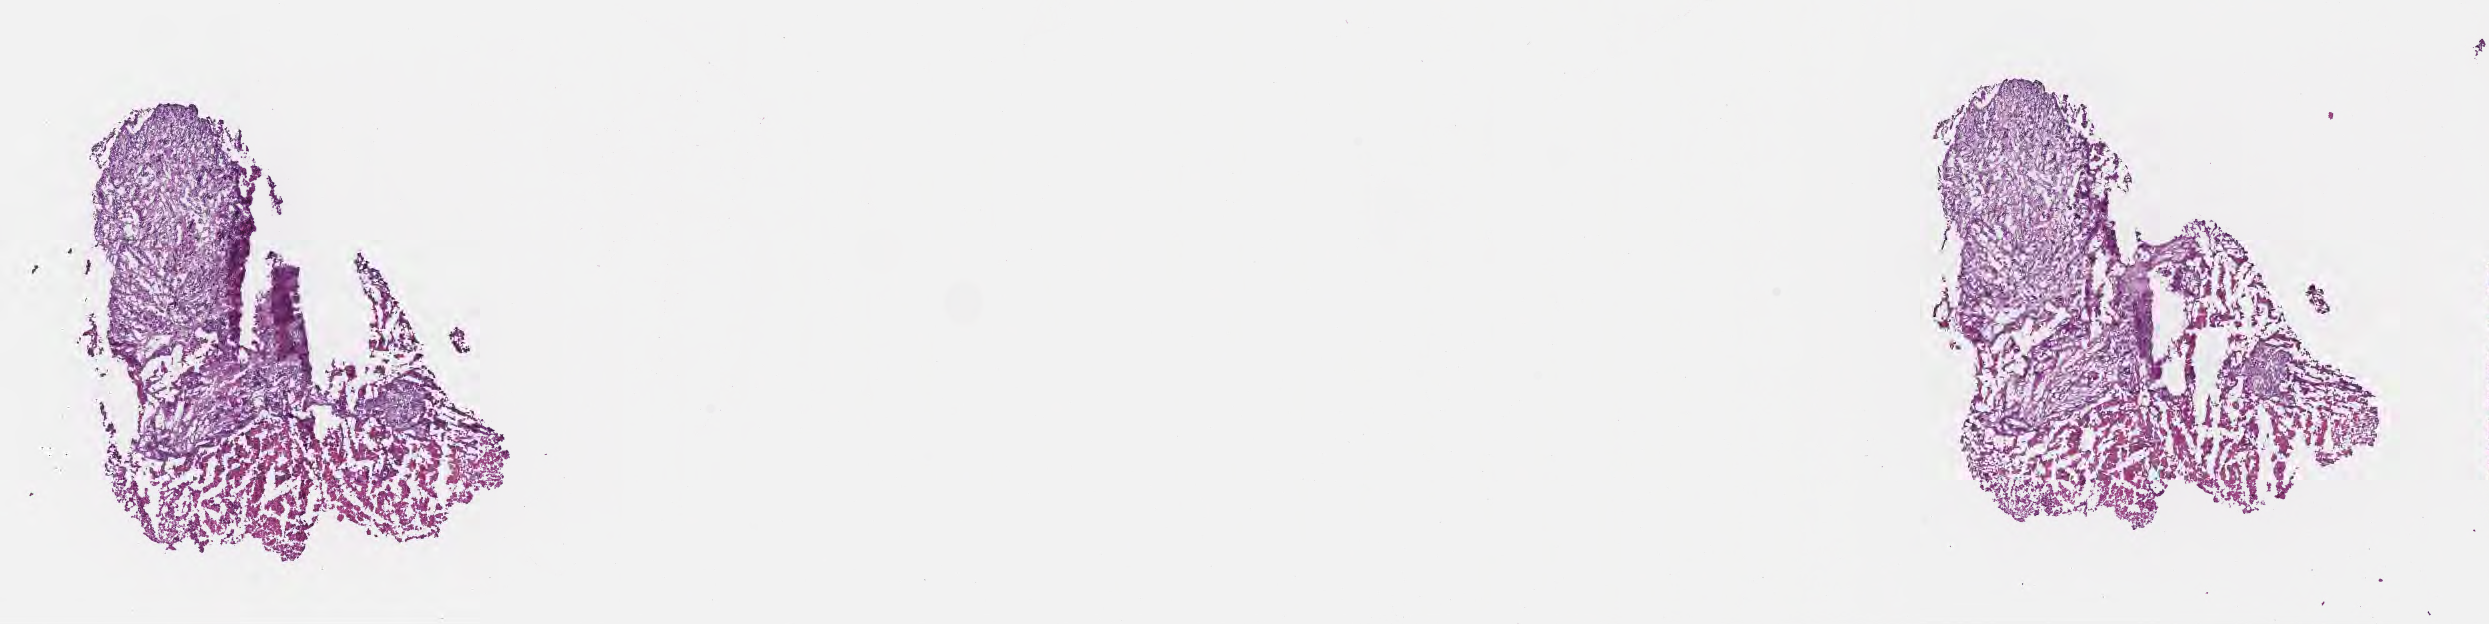
Digitized haematoxylin and eosin-stained section — shown as a low-resolution overview of the whole scanned area (about 20.1 x 5.0 mm); frozen section; metastatic tumor tissue, resected from brain. Patient: male, age at initial diagnosis 65 years. Composition of this section per pathologist review: tumor cells 70%, tumor nuclei 90%, stromal cells 5%, necrosis 25%, normal cells 0%. Inflammatory infiltration, as recorded: lymphocyte infiltration 0%, monocyte infiltration 0%, neutrophil infiltration 0%.
Patient diagnosis (primary): Small cell carcinoma, NOS.